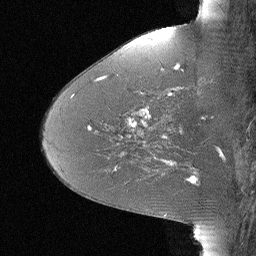
Breast MRI (dynamic contrast-enhanced), one sagittal slice; slice 25 of 64 in the series (ordered by position); dynamic contrast-enhanced study with each time point stored as its own series, time point 2 of 3 at this slice position (early post-contrast, ordered by acquisition time); 1.5 T; TE 4 ms, TR 30 ms; 2.25 mm slice thickness; 256 × 256 image matrix, field of view 180 × 180 mm. Patient: female, 46 years. Case-level facts recorded for this patient, not image findings: setting: breast cancer imaged before/during neoadjuvant chemotherapy; receptor status: HR-positive, HER2-negative.
Outlined on this slice (semi-automatically segmented with operator editing):
- analysis volume of interest (the breast-tissue region the enhancement analysis was run in; not a lesion): bounding box (x1, y1, x2, y2) in pixels: (106, 43, 184, 119)
- tumour enhancement mask (voxels above the 90 % enhancement threshold inside the analysis volume of interest): (129, 66, 178, 119)